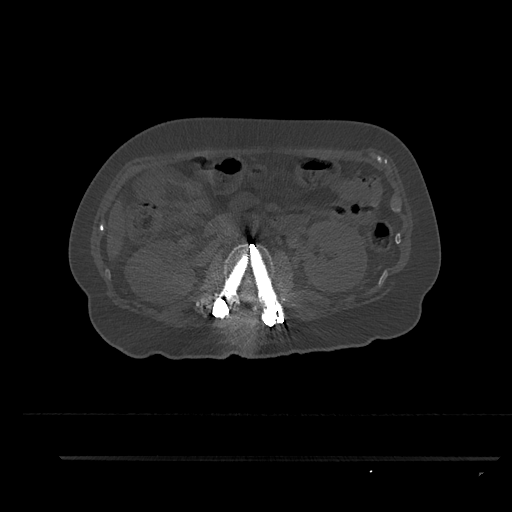
CT including the spine, one axial slice; position 171 of 797 along the scan axis; reconstruction kernel Br40s/3; bone window (W 1800 / L 400 HU); 512 × 512 image matrix, field of view 408 × 408 mm. Patient: female, 44 years. Case-level facts recorded for this patient, not image findings: primary cancer: renal.
Outlined on this slice (semi-automatic segmentation, software-assisted and operator-edited):
- L2 vertebra: bounding box [x1, y1, x2, y2] px = [209, 243, 284, 319]